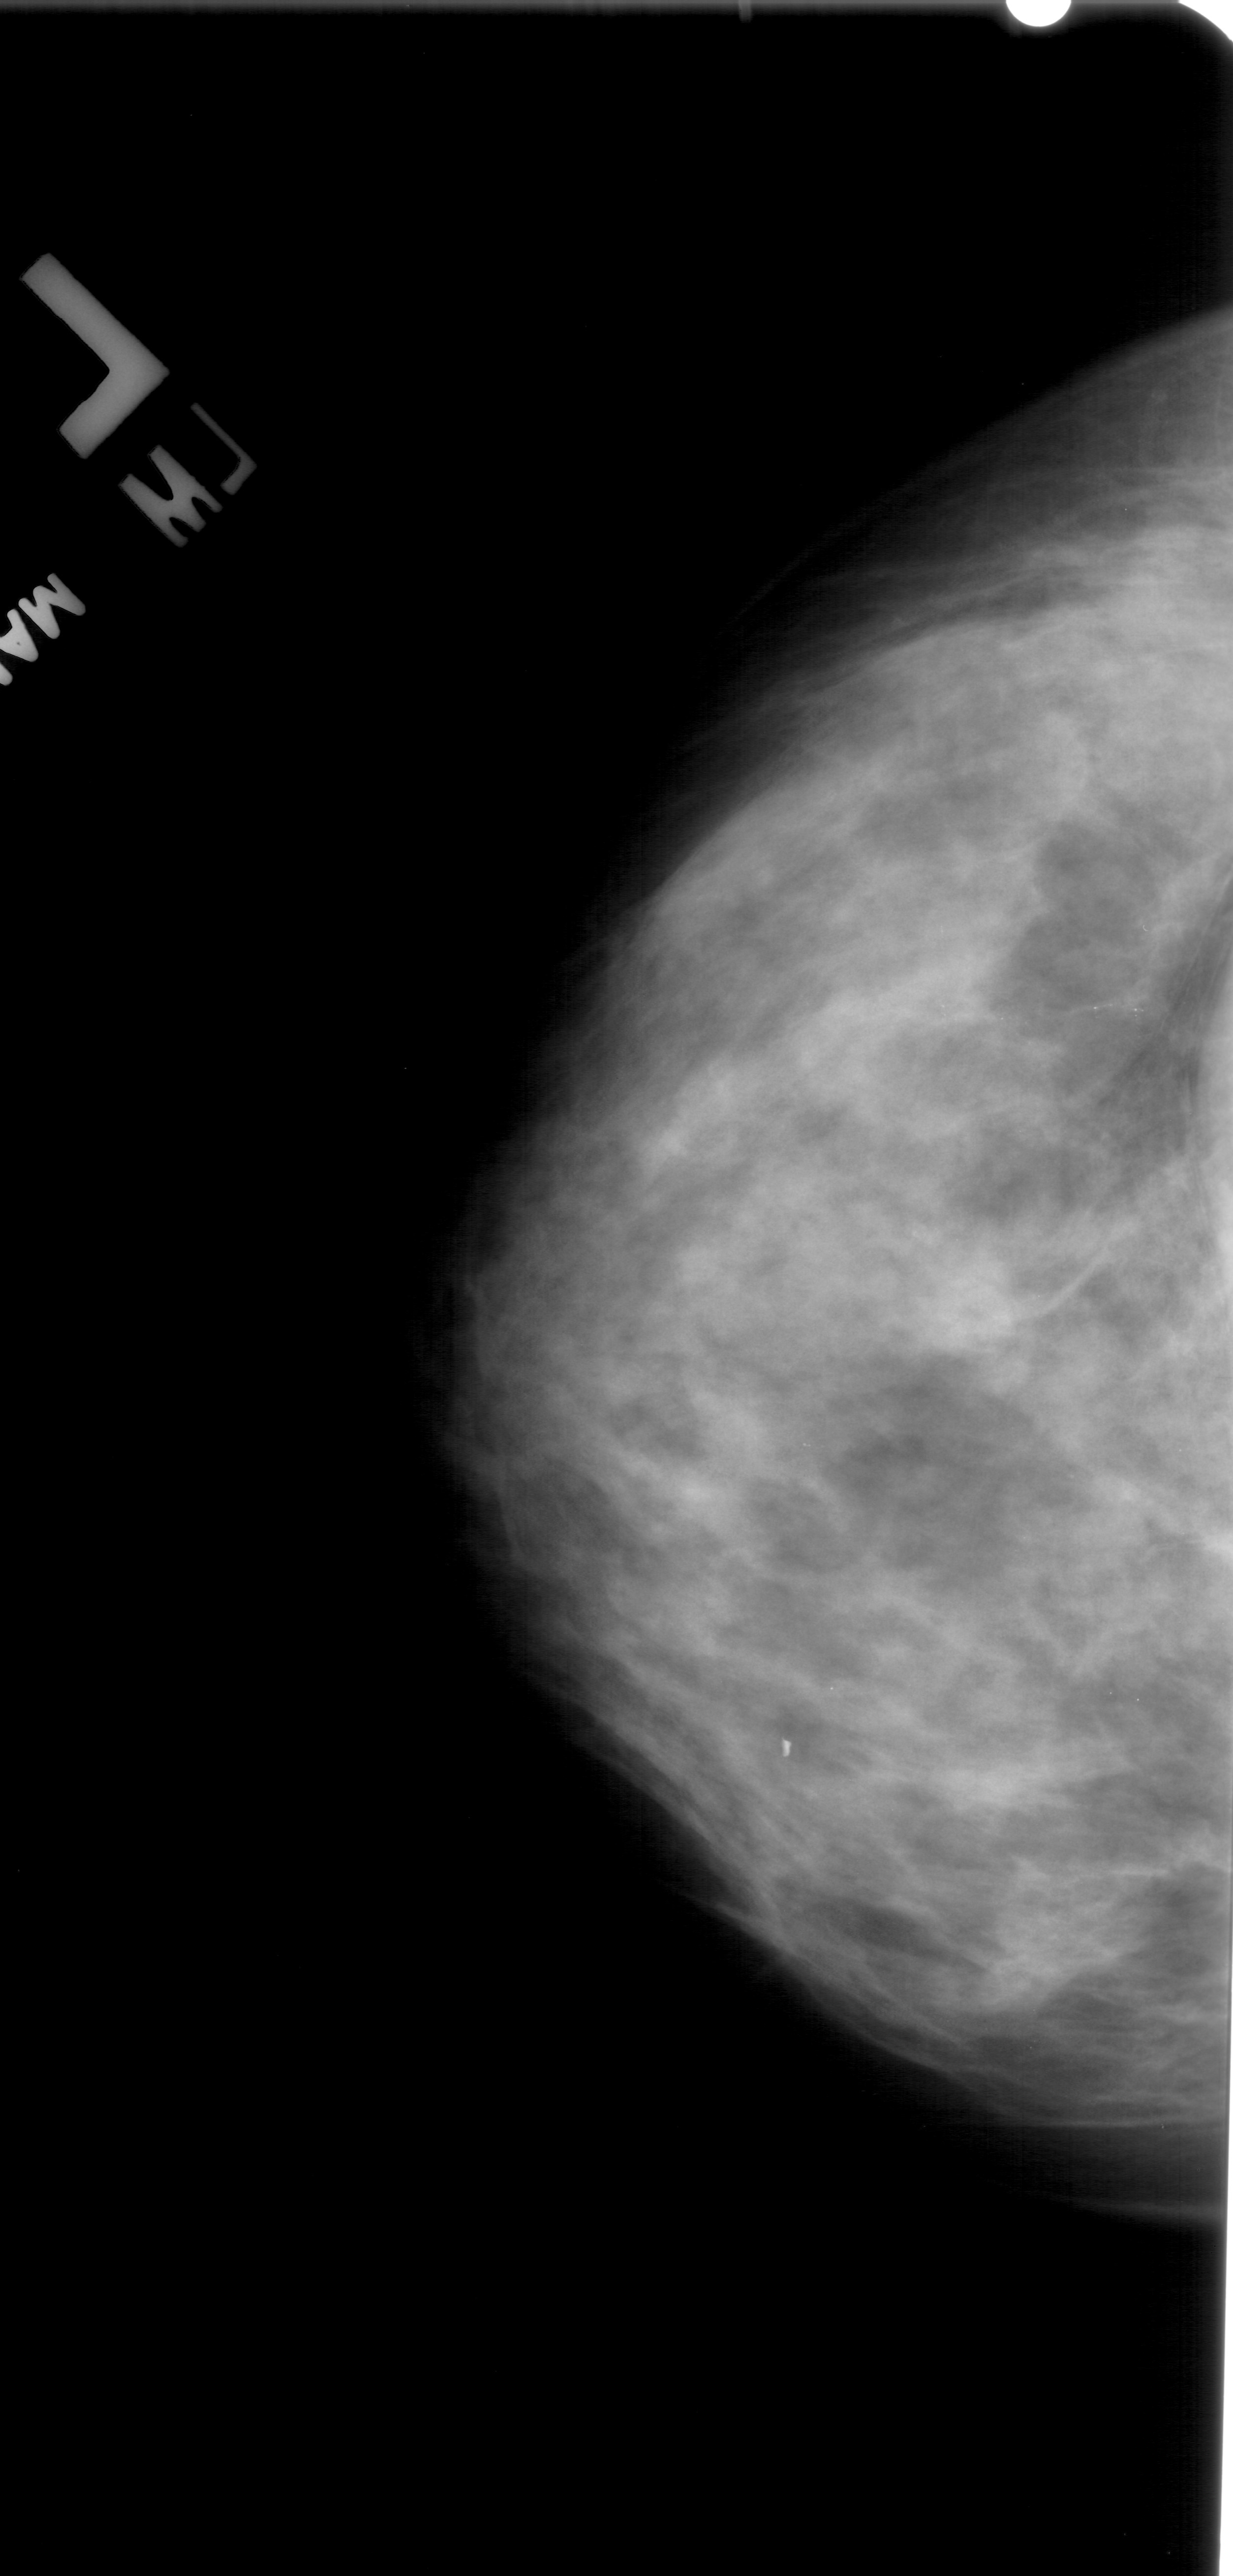
Mammogram (digitized film); left breast; CC view; BI-RADS breast density category 4 (scale 1–4); 1233 × 2576 image matrix.
Marked abnormalities (boxes around the expert regions of interest):
- calcifications, morphology pleomorphic, distribution clustered; BI-RADS assessment category 4; subtlety rating 1 on a 1 (subtle) to 5 (obvious) scale; pathology result (as recorded, not read from the image): benign: bounding box <897,1206,973,1255> (left, top, right, bottom; pixels)